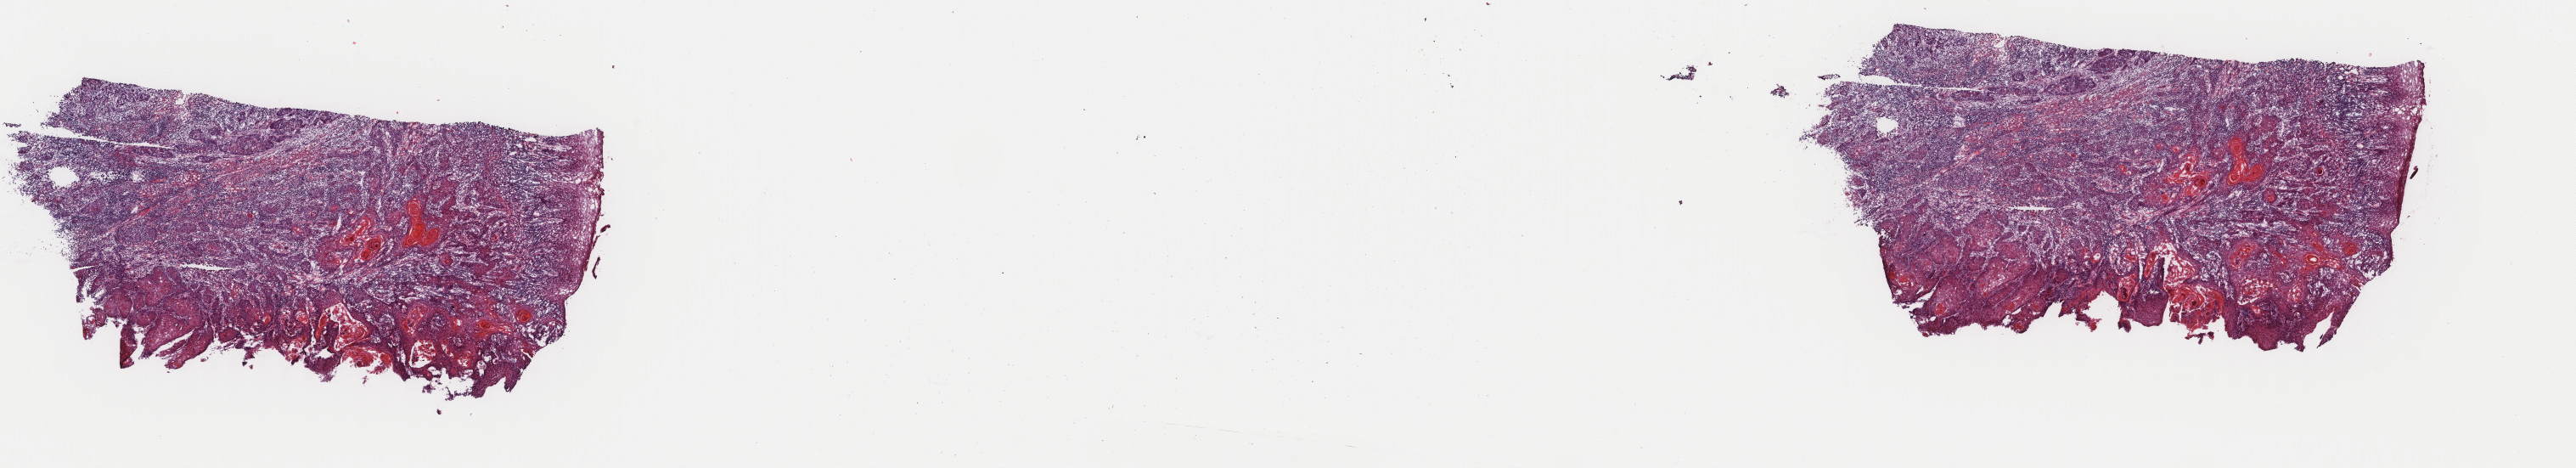
Hematoxylin and eosin (H&E) stained whole-slide image — shown as a low-resolution overview of the whole scanned area (about 24.1 x 4.4 mm); frozen section from the top of the tissue portion; sample: primary tumour, head and neck. Female, age 45 years at initial diagnosis. Histologic grade: G1 (well differentiated). Composition of this section per pathologist review: tumour cells 98%, tumour nuclei 70%, normal cells 2%, stromal cells 0%, necrosis 0%. Inflammatory infiltration, as recorded: lymphocyte infiltration 10%, monocyte infiltration 0%, neutrophil infiltration 1%.
AJCC pathologic stage: III (7th edition). Diagnosis: Squamous cell carcinoma, NOS (tongue, NOS). TNM: T3 N0 M0.